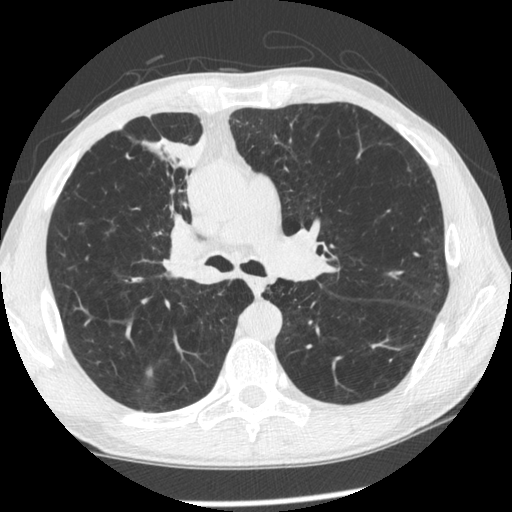
Low-dose screening chest CT, one axial slice; slice 144 of 261 in the series (ordered by position); lung window (W 1500 / L -600 HU); 1.25 mm slice thickness; 512 × 512 image matrix.
Structures marked on this image (expert manual segmentation):
- lesion 1 (tumor, upper lobe of right lung): bounding box (x1, y1, x2, y2) in pixels: (144, 135, 206, 236)